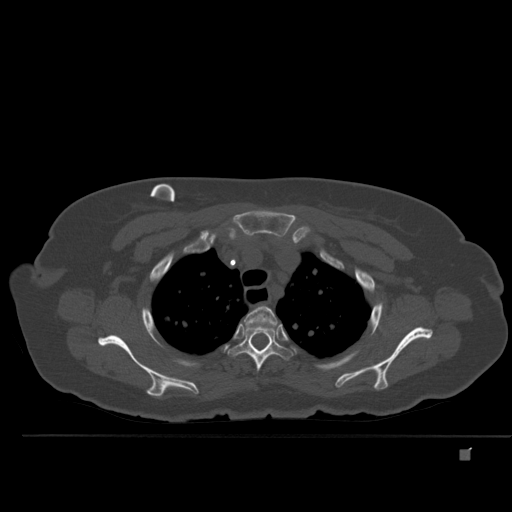
CT including the spine, one axial slice. Position 382 of 477 along the scan axis. Bone window (W 1800 / L 400 HU). 1.5 mm slice thickness. 512 × 512 image matrix, field of view 422 × 422 mm. Patient: female, 74 years. Case-level facts recorded for this patient, not image findings: primary cancer: colon.
Structures marked on this image (semi-automatically segmented with operator editing):
- T2 vertebra: bounding box <244,306,277,327> (left, top, right, bottom; pixels)
- T3 vertebra: <228,322,293,371>